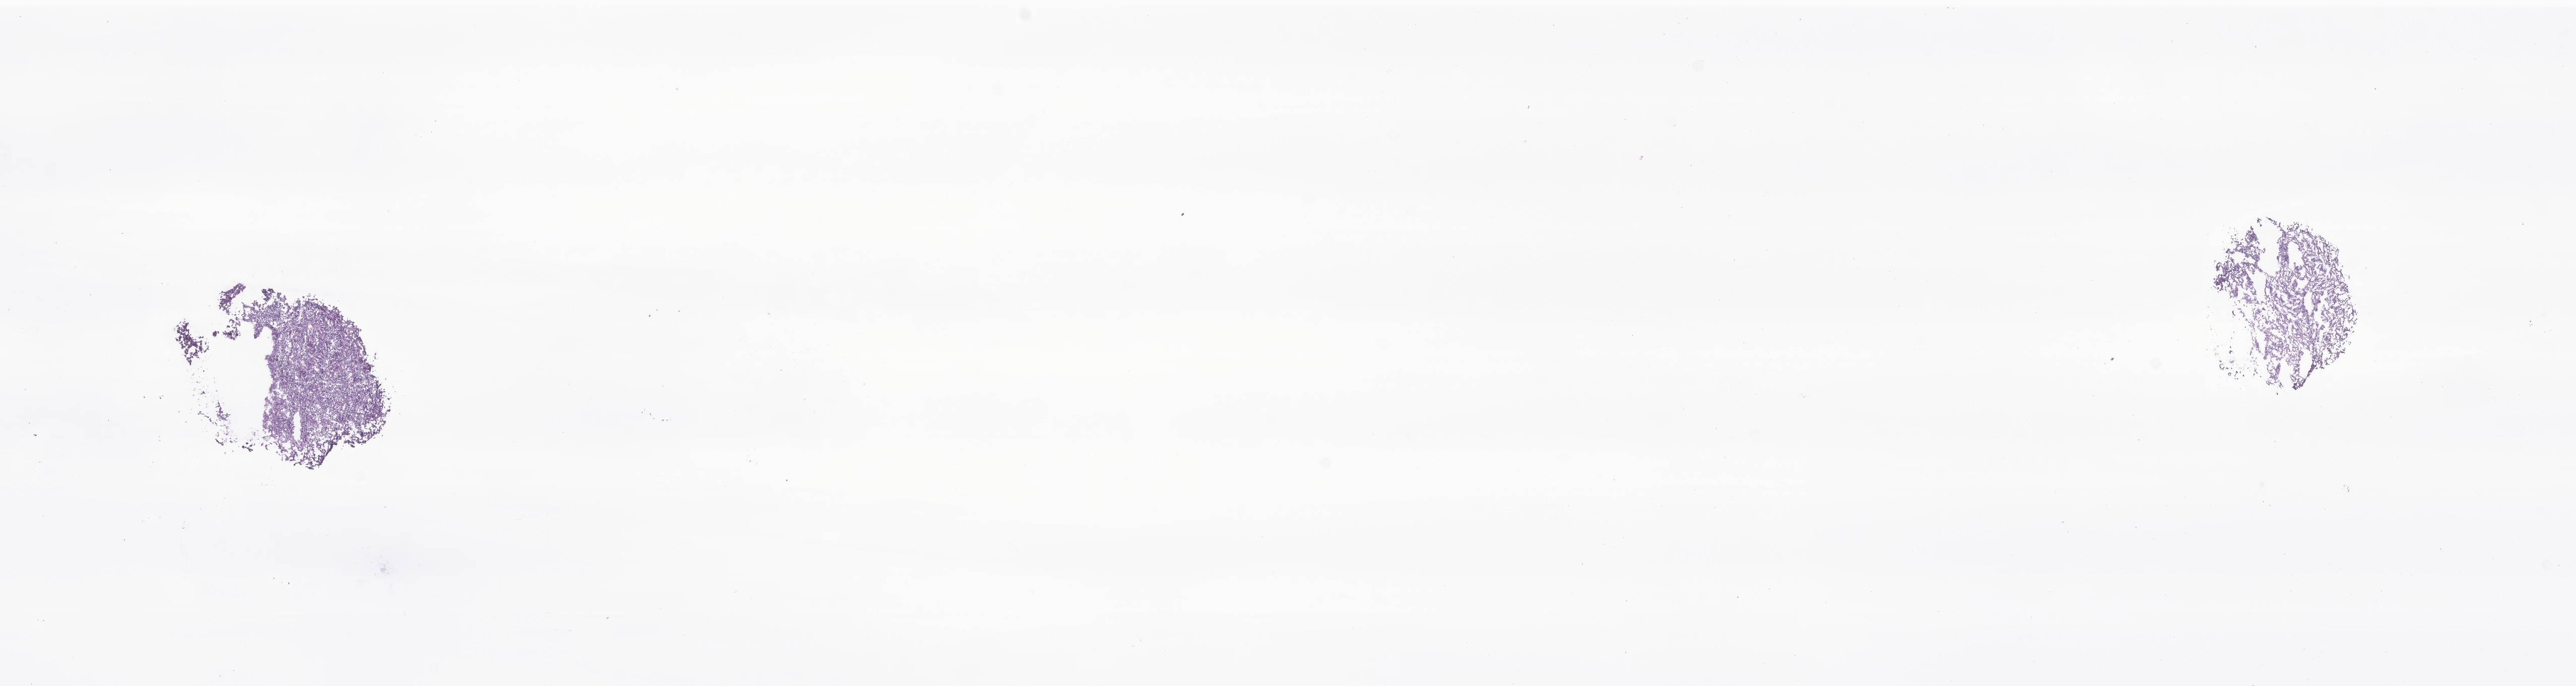
Hematoxylin and eosin (H&E) whole-slide image of tumor tissue from the brain — a low-resolution overview of the entire scanned area, about 21.5 x 5.7 mm. Frozen section. Patient: female, age 41 months (3 years 5 months).
• diagnosis: Medulloblastoma, NOS